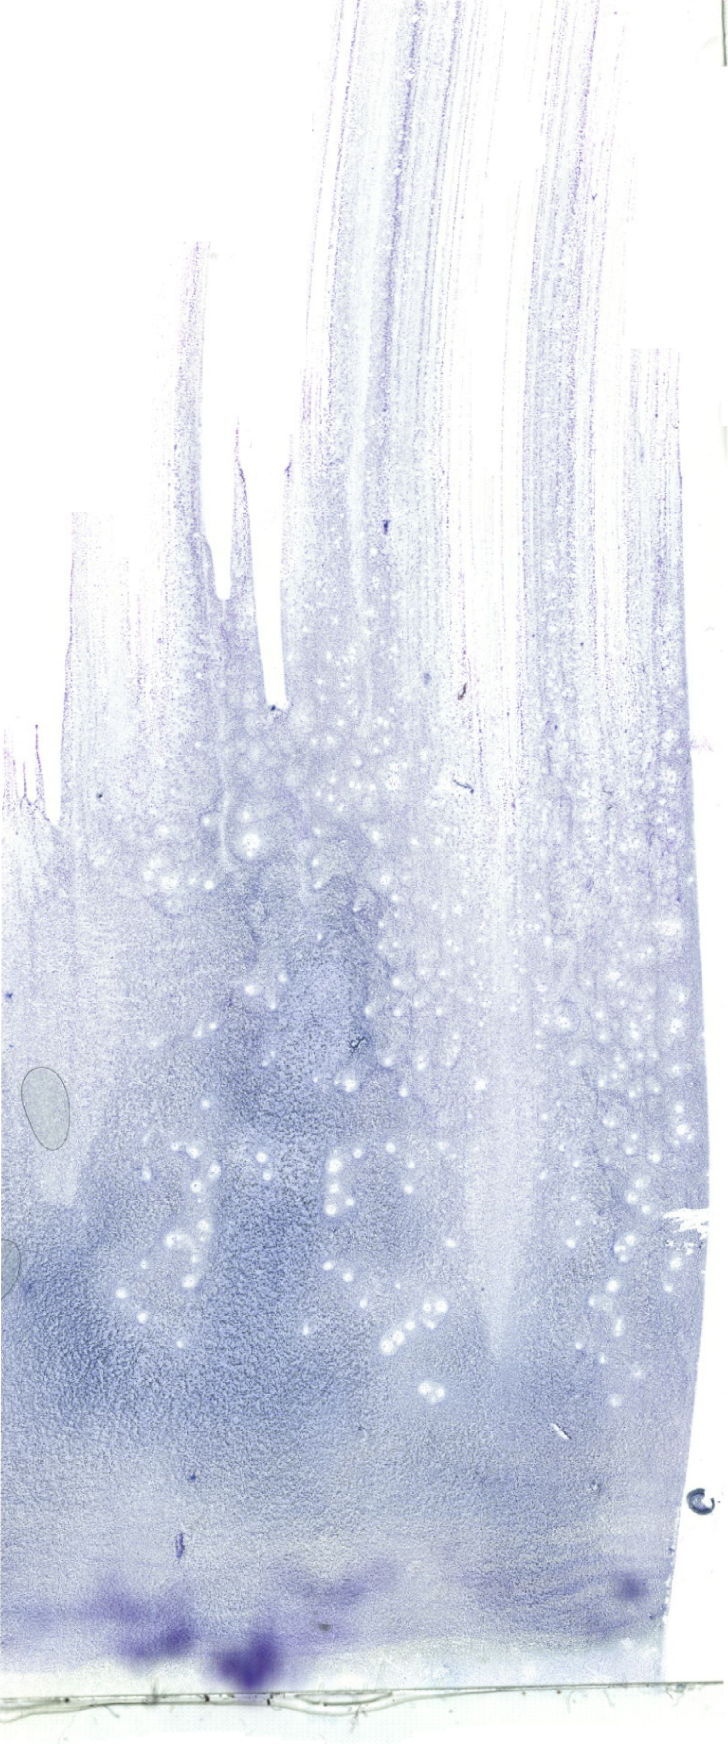
May-Grünwald–Giemsa-stained marrow aspirate smear (whole slide) — low-resolution overview of the scanned area, about 20.6 x 49.4 mm. Patient sex: female.
Diagnosis: B Acute Lymphoblastic Leukemia.